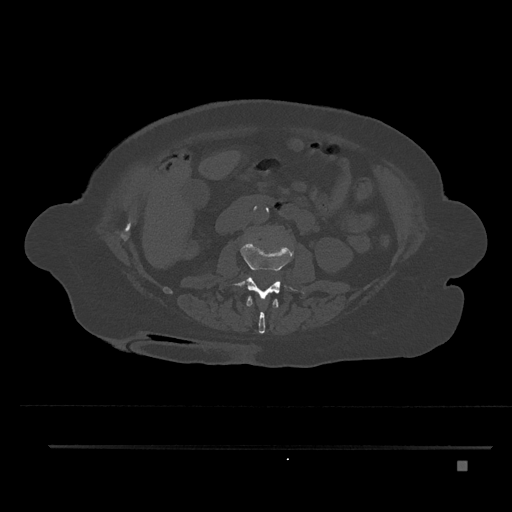
CT including the spine, one axial slice; slice 173 of 797 in the series (ordered by position); reconstruction kernel Br40s/3; 120 kVp; bone window (W 1800 / L 400 HU); 0.5 mm slice thickness; 512 × 512 image matrix. Patient: female, 76 years. Case-level facts recorded for this patient, not image findings: primary cancer: lung; vertebrae with lytic lesions (as recorded): T11, L3.
Outlined on this slice (semi-automatic segmentation, software-assisted and operator-edited):
- L1 vertebra: box from (x=246, y=296) to (x=279, y=334) px
- L2 vertebra: (x=232, y=242)–(x=305, y=303)